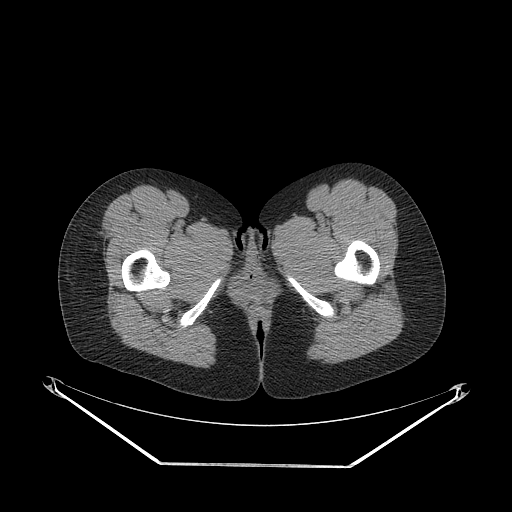
CT of an extremity soft-tissue mass (from a PET/CT study), one axial slice. Position 48 of 267 along the scan axis. Reconstruction kernel STANDARD. Soft-tissue window (W 400 / L 40 HU). 3.75 mm slice thickness. 512 × 512 image matrix, field of view 500 × 500 mm. Female patient. Case-level facts recorded for this patient, not image findings: histological type: synovial sarcoma; grade: intermediate; site of the primary tumour: right thigh.
Structures marked on this image (expert contour drawn on MRI and transferred to this co-registered scan by the dataset authors):
- gross tumour volume including surrounding oedema: bounding box [x1, y1, x2, y2] px = [98, 226, 104, 236]
- gross tumour volume (mass): [96, 226, 104, 236]